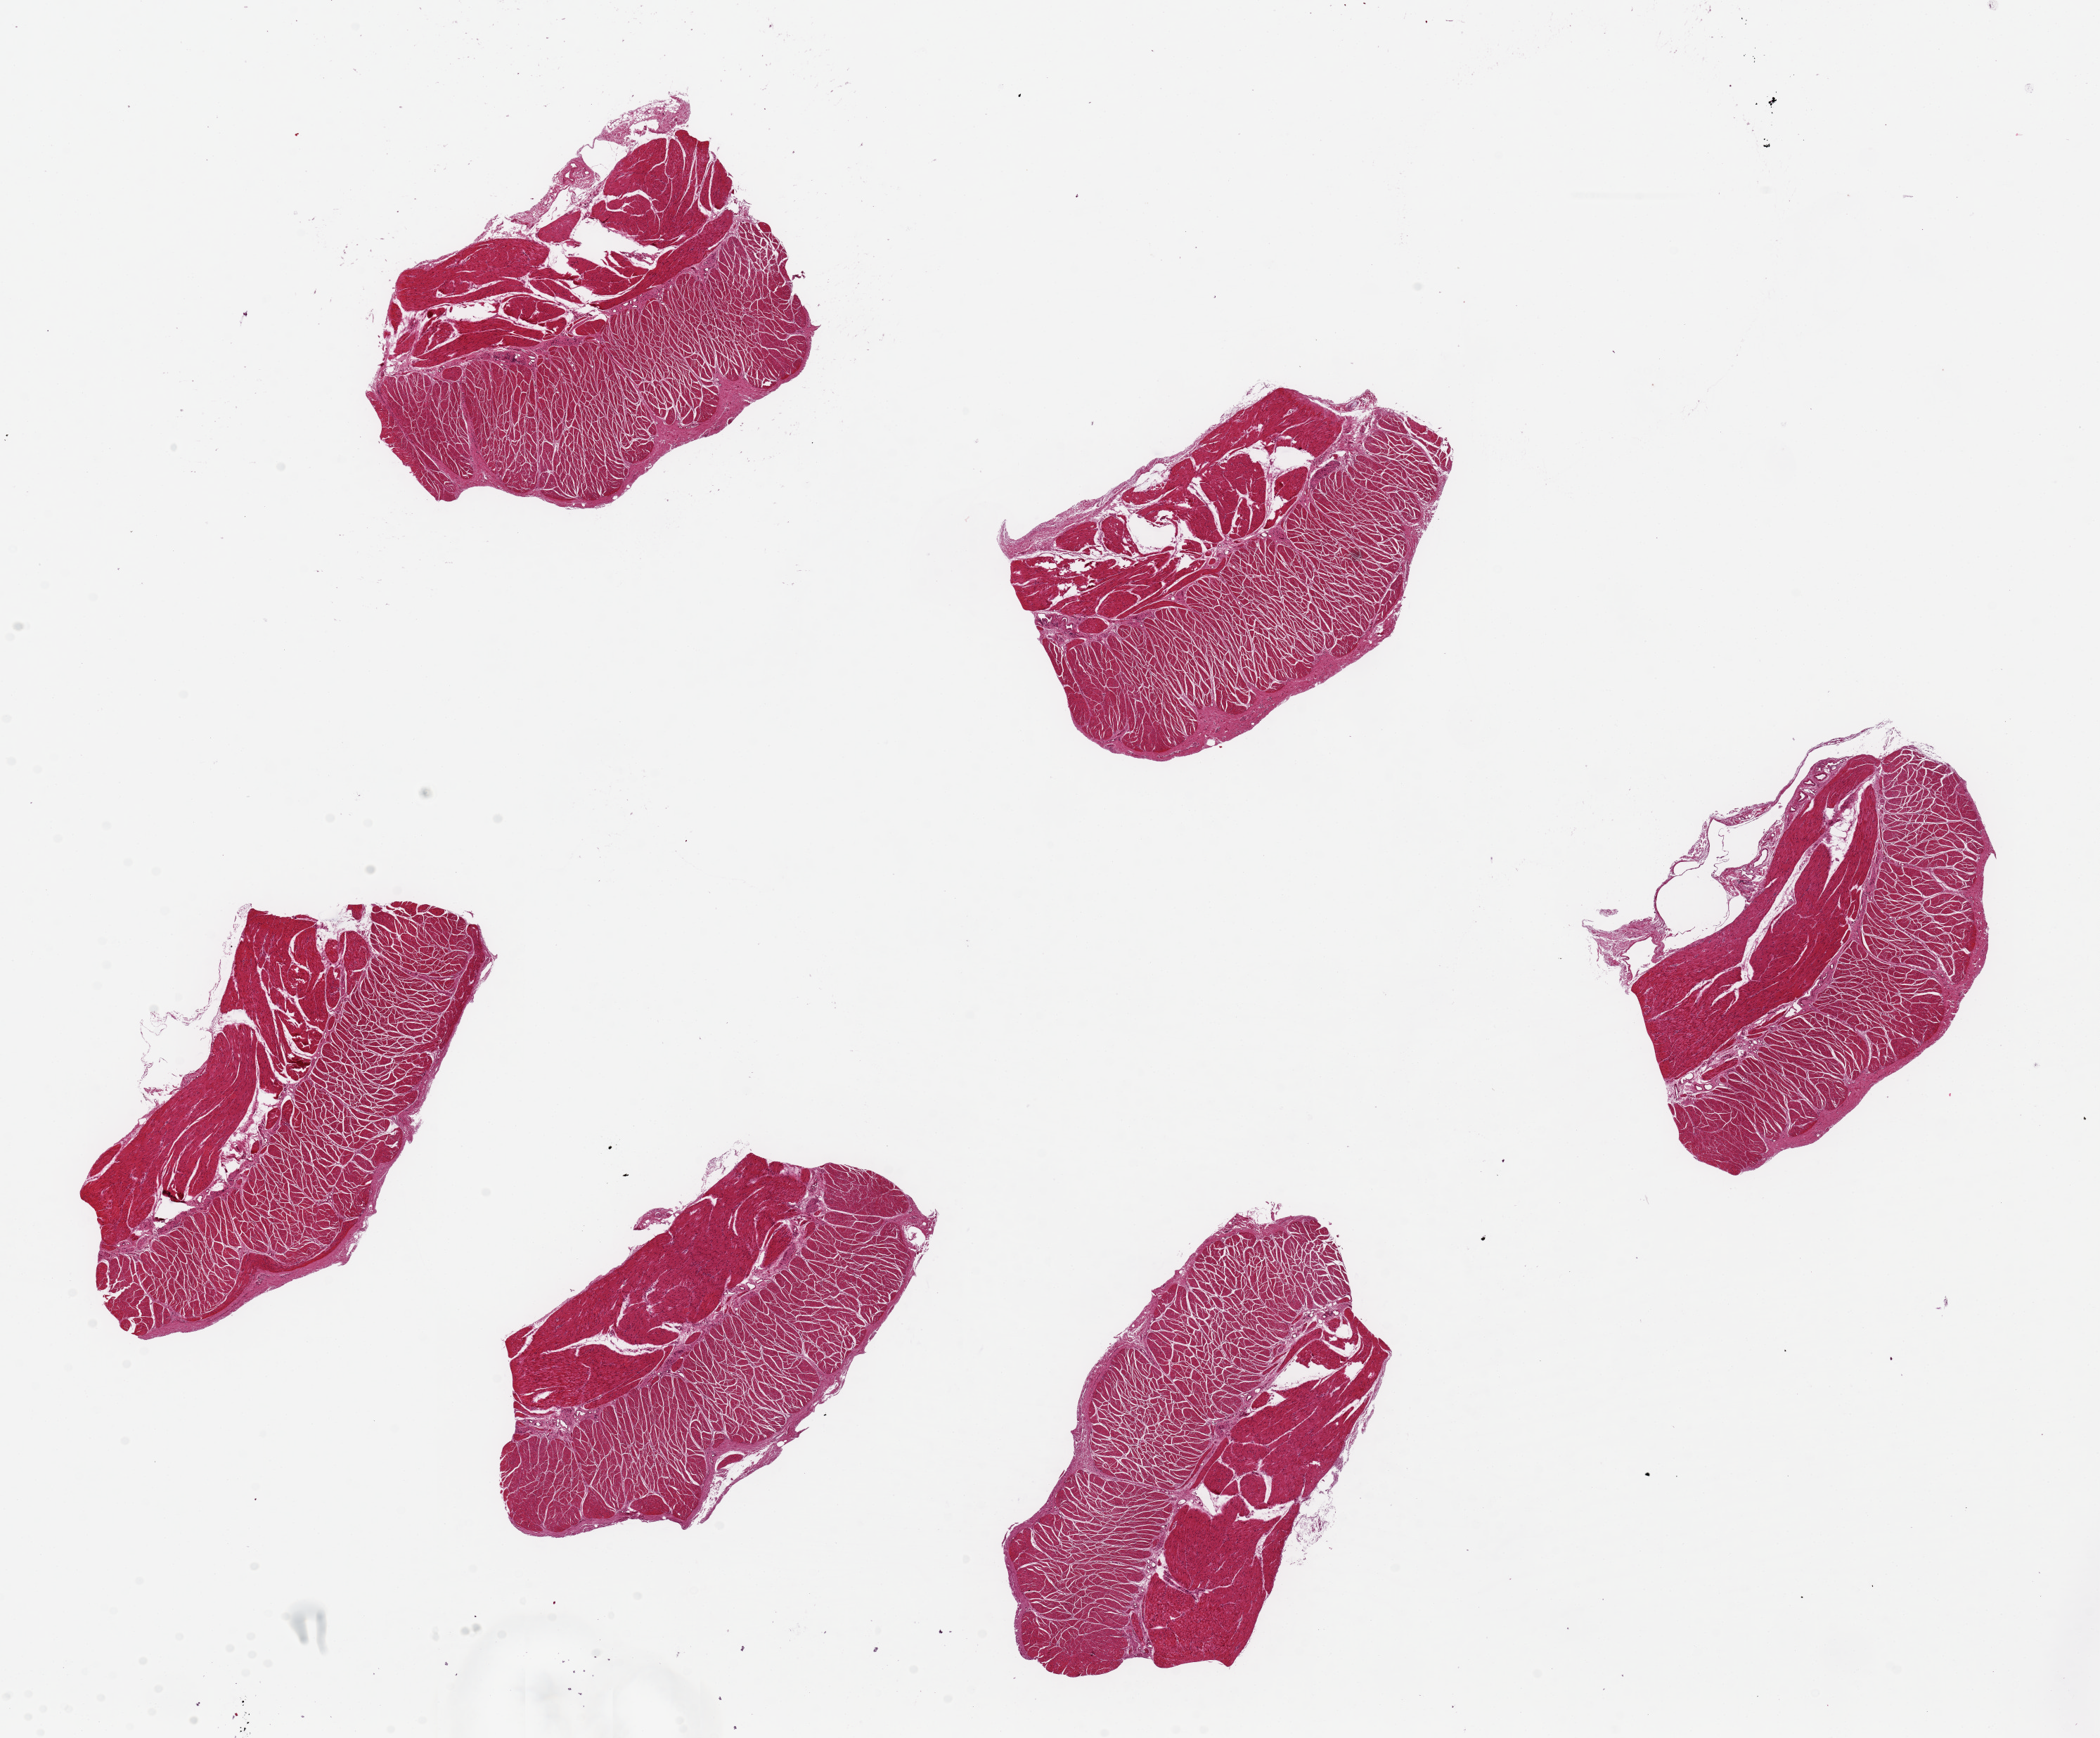
Whole-slide image, hematoxylin and eosin (H&E) stain, brightfield — low-resolution overview of the scanned area, about 23.6 x 19.6 mm (slide scanned at 20x), PAXgene-fixed paraffin-embedded (PFPE) section, sampled site (target tissue): esophageal muscle, donor tissue sample. Donor sex: female.
Review note (as recorded): 6 pieces up to 6x3 mm.